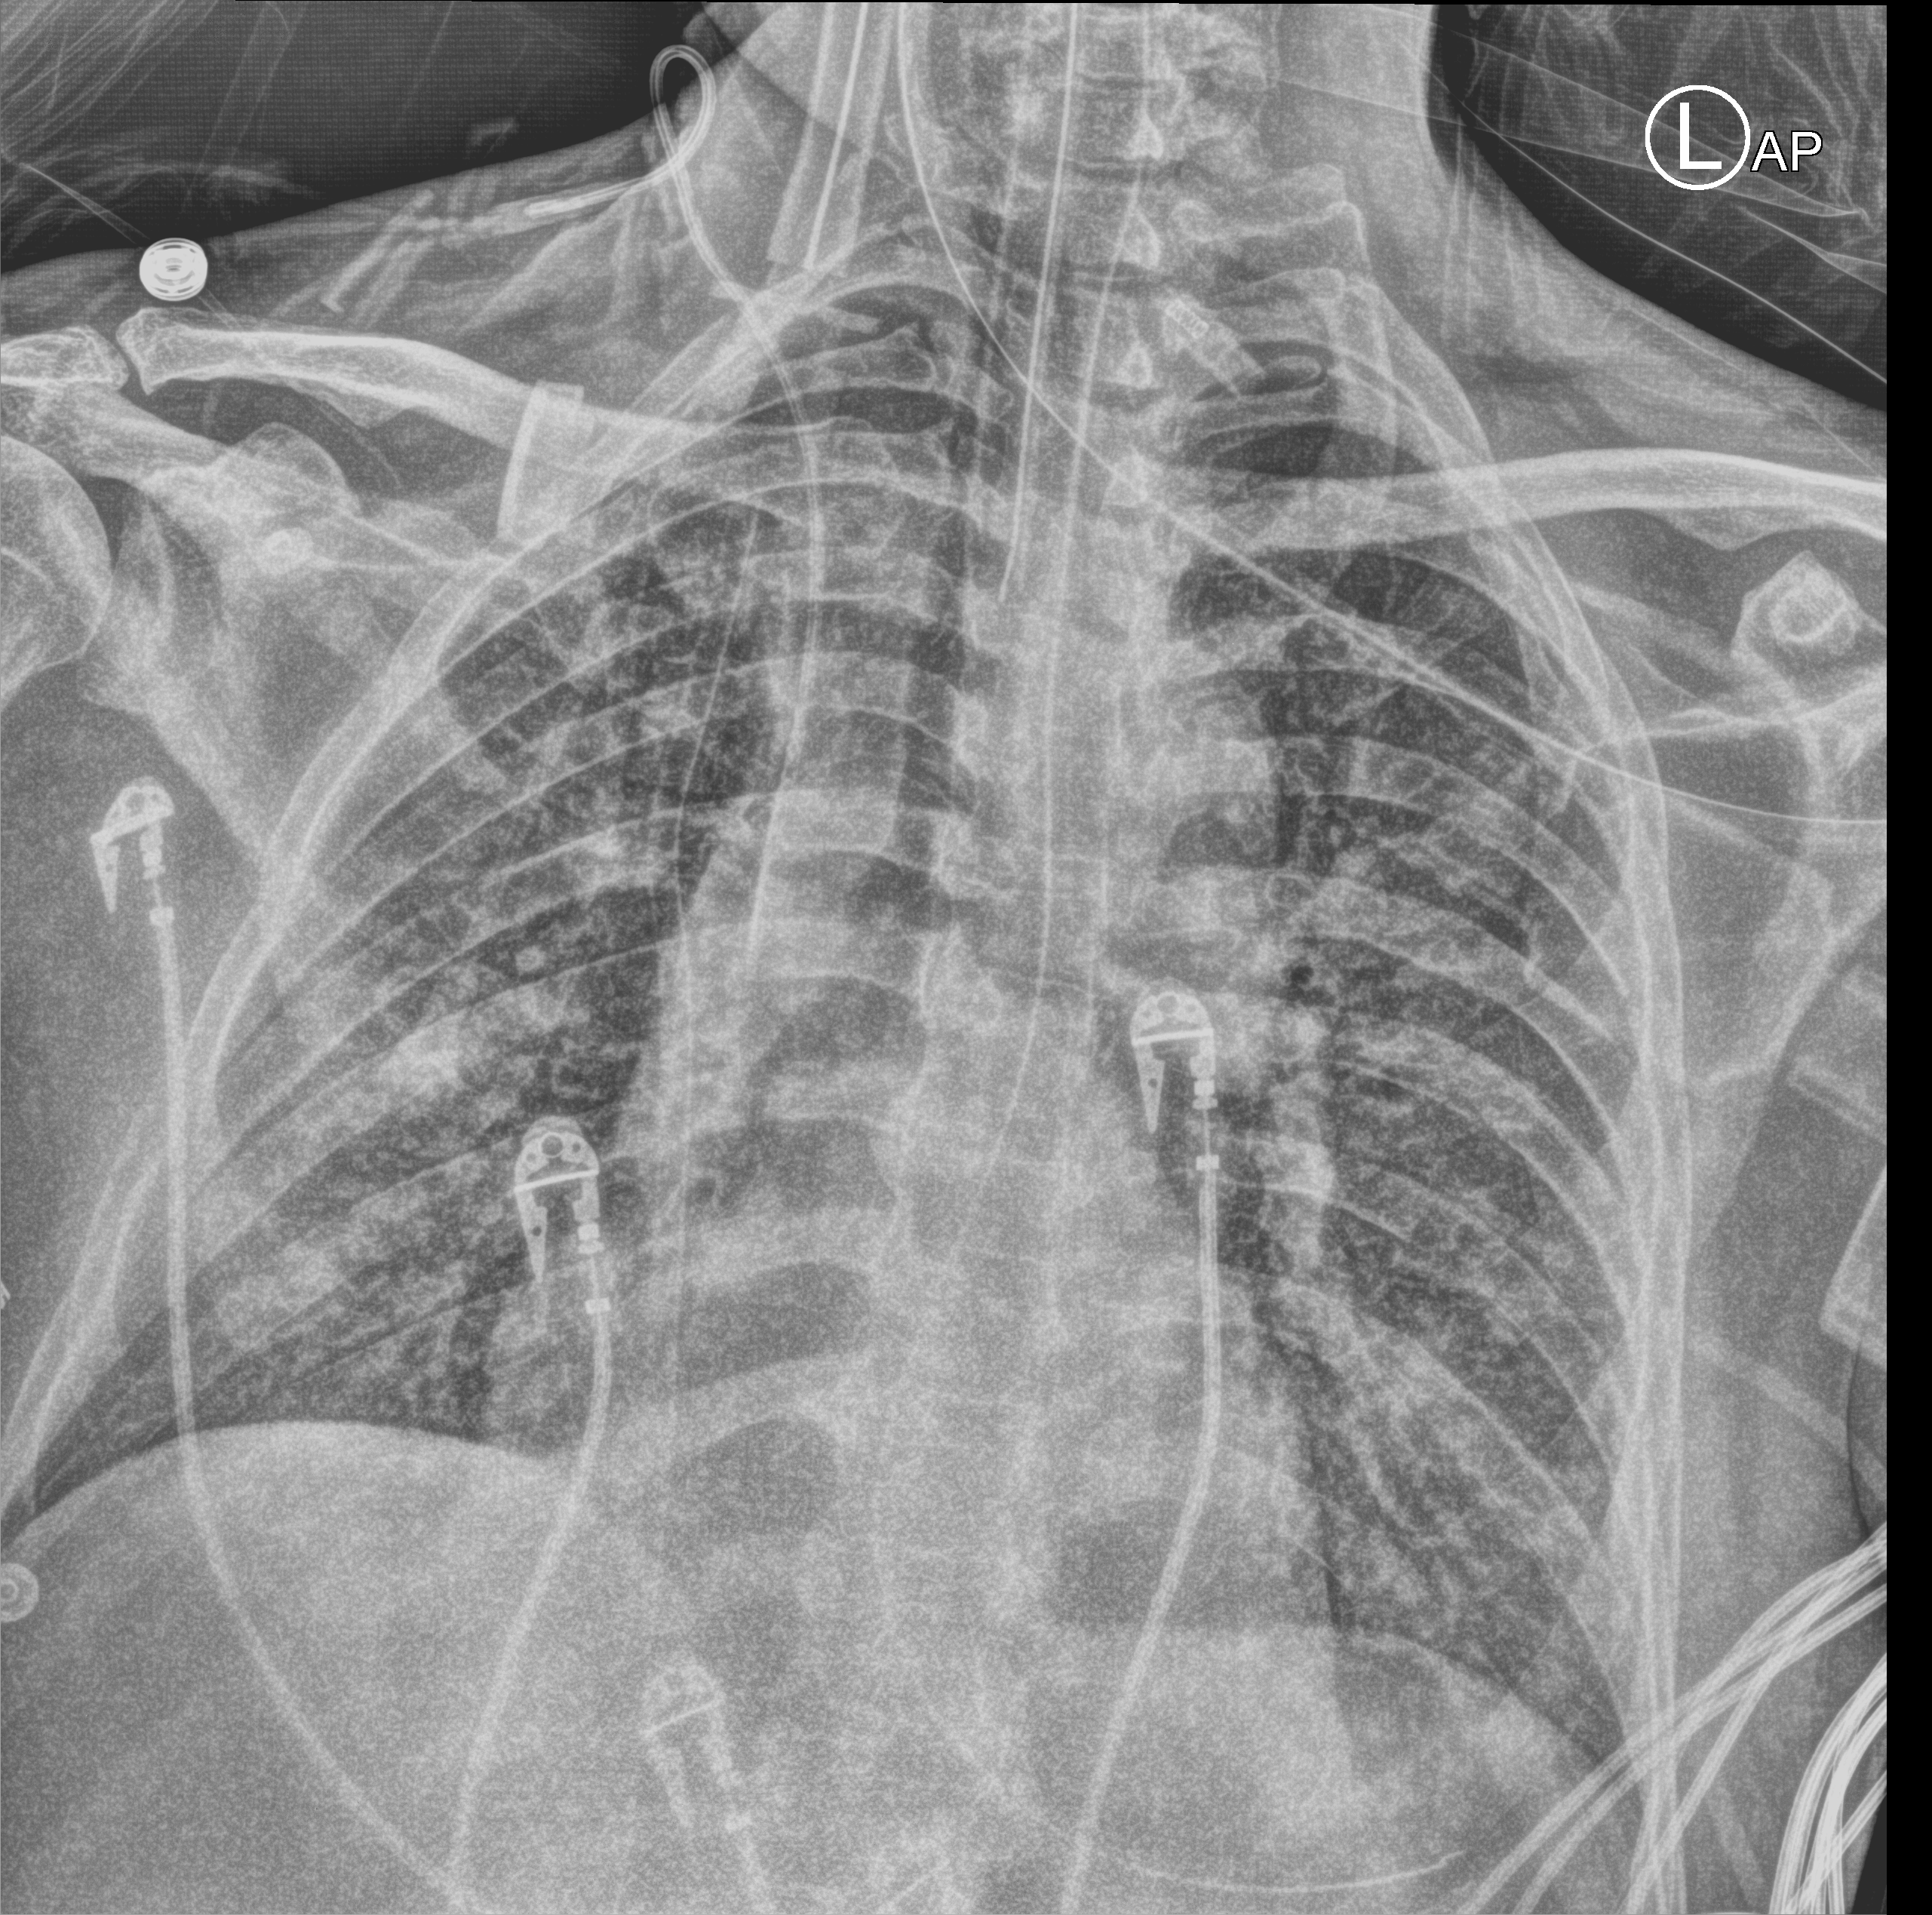
Portable chest radiograph; anteroposterior (AP) projection. Patient hospitalised with COVID-19; male, aged 60–74 years.
From the hospital-stay record, not from the radiograph (when in the stay this image was taken is not recorded): admitted to intensive care during this hospital stay: yes; COPD (admission record): no.